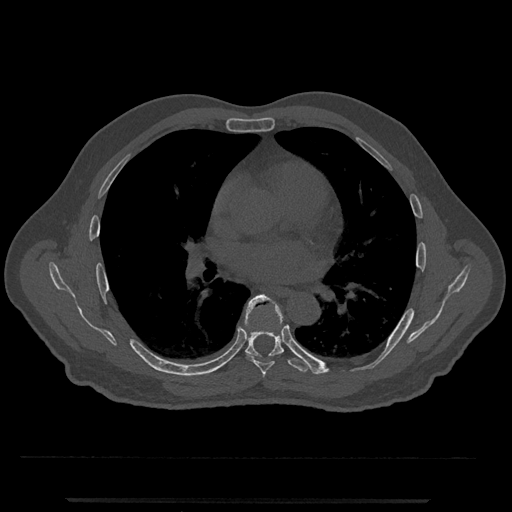
CT including the spine, one axial slice; position 712 of 797 along the scan axis; bone window (W 1800 / L 400 HU); 0.5 mm slice thickness; 512 × 512 image matrix. Male patient, age 63 years. From the clinical record (not read from this slice): primary cancer: prostate.
Outlined on this slice (semi-automatically segmented with operator editing):
- T5 vertebra: bounding box (x1, y1, x2, y2) in pixels: (262, 374, 264, 377)
- T6 vertebra: (245, 295, 283, 376)
- T7 vertebra: (221, 303, 324, 374)